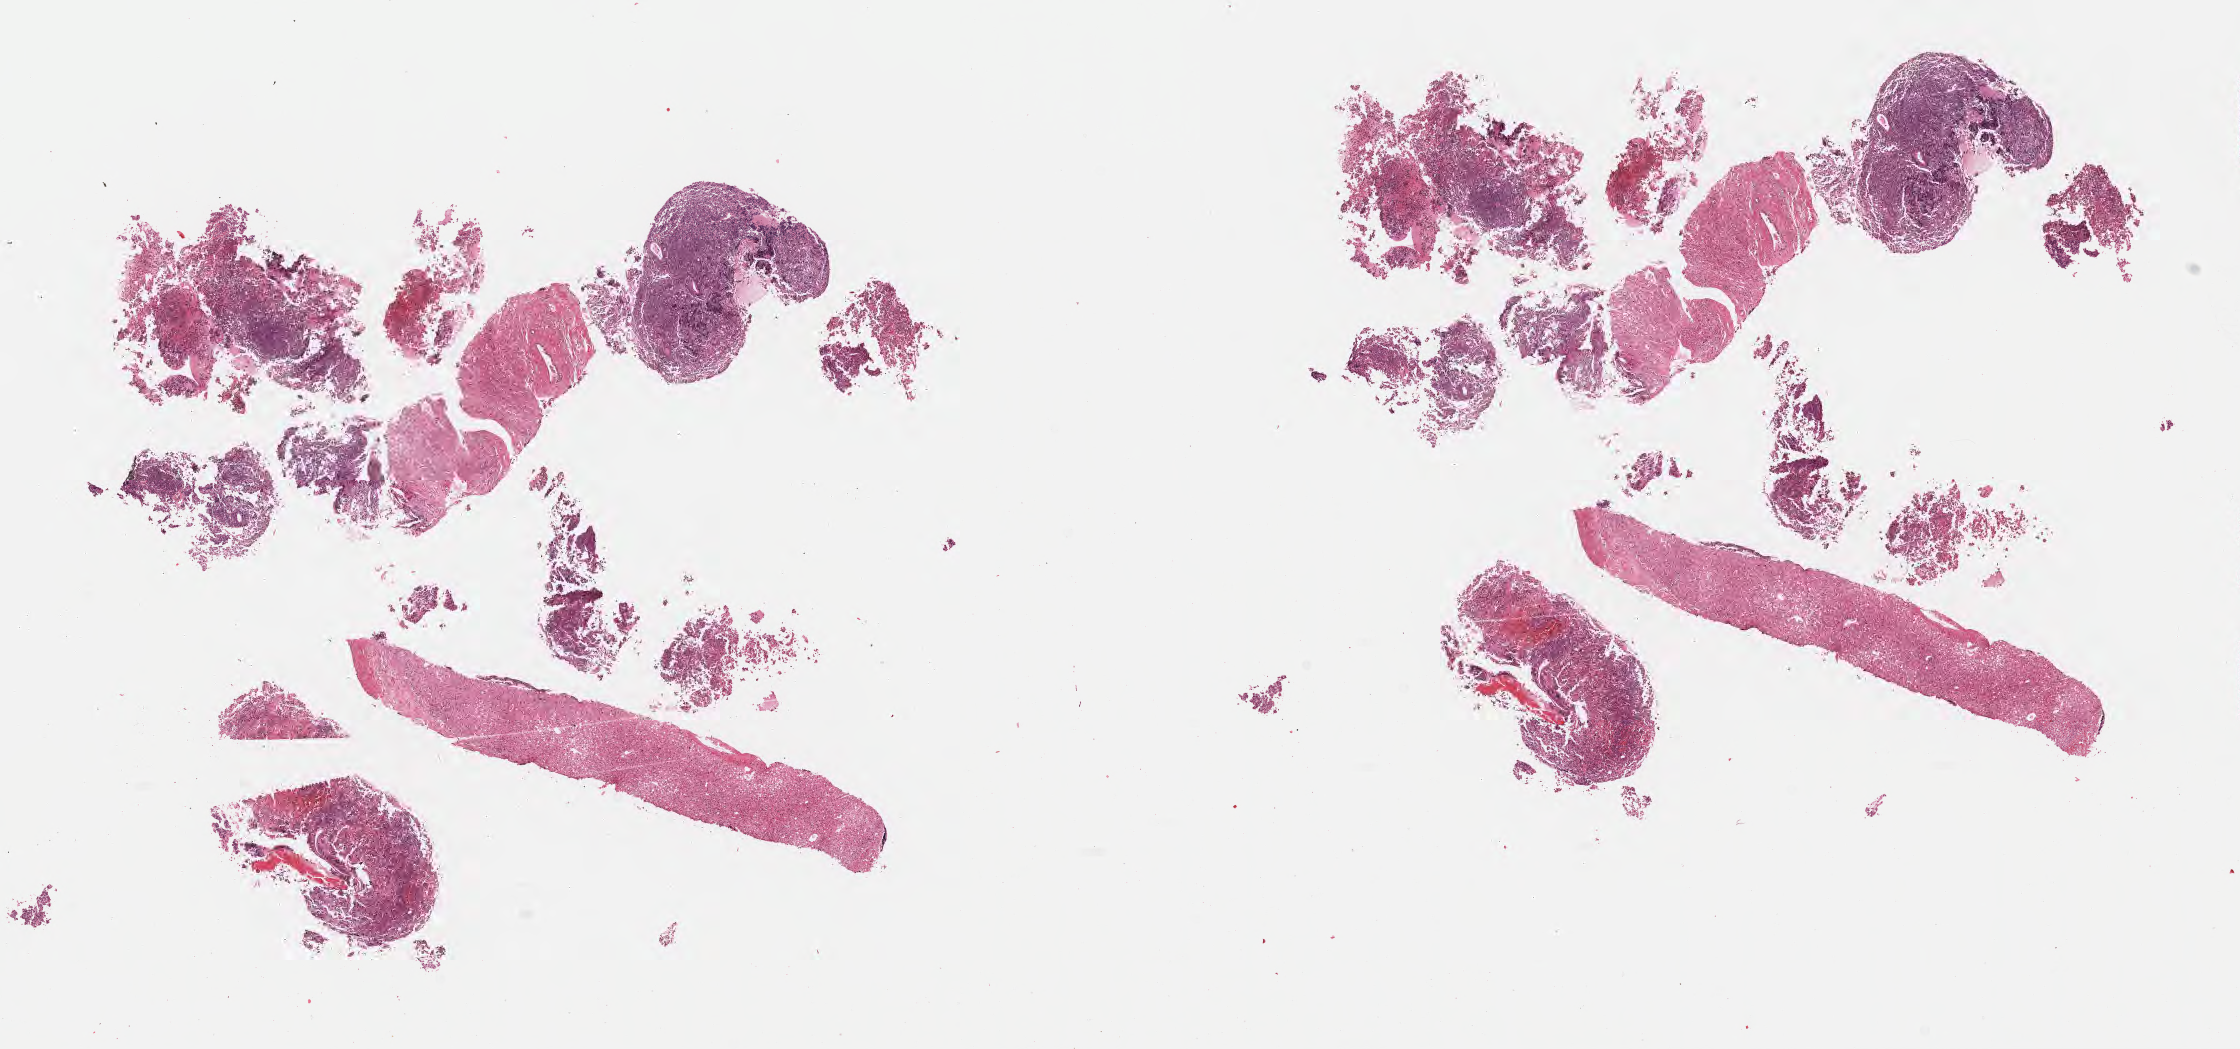
Digitized haematoxylin and eosin-stained section — low-resolution overview of the scanned area, about 18.1 x 8.5 mm. Formalin-fixed paraffin-embedded section. Primary tumor. Site: liver. Patient: male, age at initial diagnosis 5 years.
Diagnosis: Burkitt lymphoma, NOS.